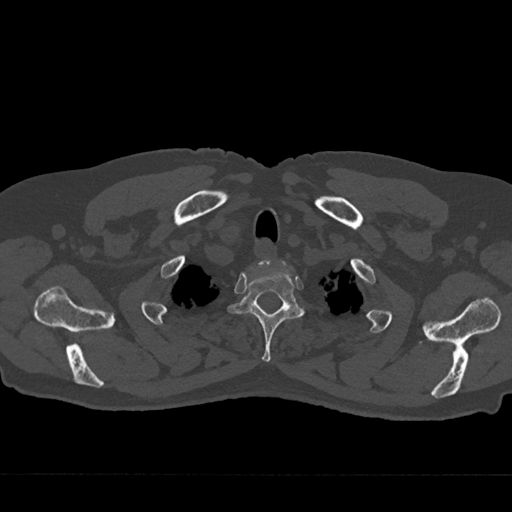
CT including the spine, one axial slice. Position 617 of 797 along the scan axis. Reconstruction kernel Br40s/3. 120 kVp. Bone window (W 1800 / L 400 HU). 0.5 mm slice thickness. 512 × 512 image matrix, field of view 377 × 377 mm. Patient: male, 75 years. Case-level facts recorded for this patient, not image findings: primary cancer: renal; vertebrae with lytic lesions (as recorded): T4.
Structures marked on this image (semi-automatically segmented with operator editing):
- T1 vertebra: bounding box <260,259,285,266> (left, top, right, bottom; pixels)
- T2 vertebra: <228,262,305,362>